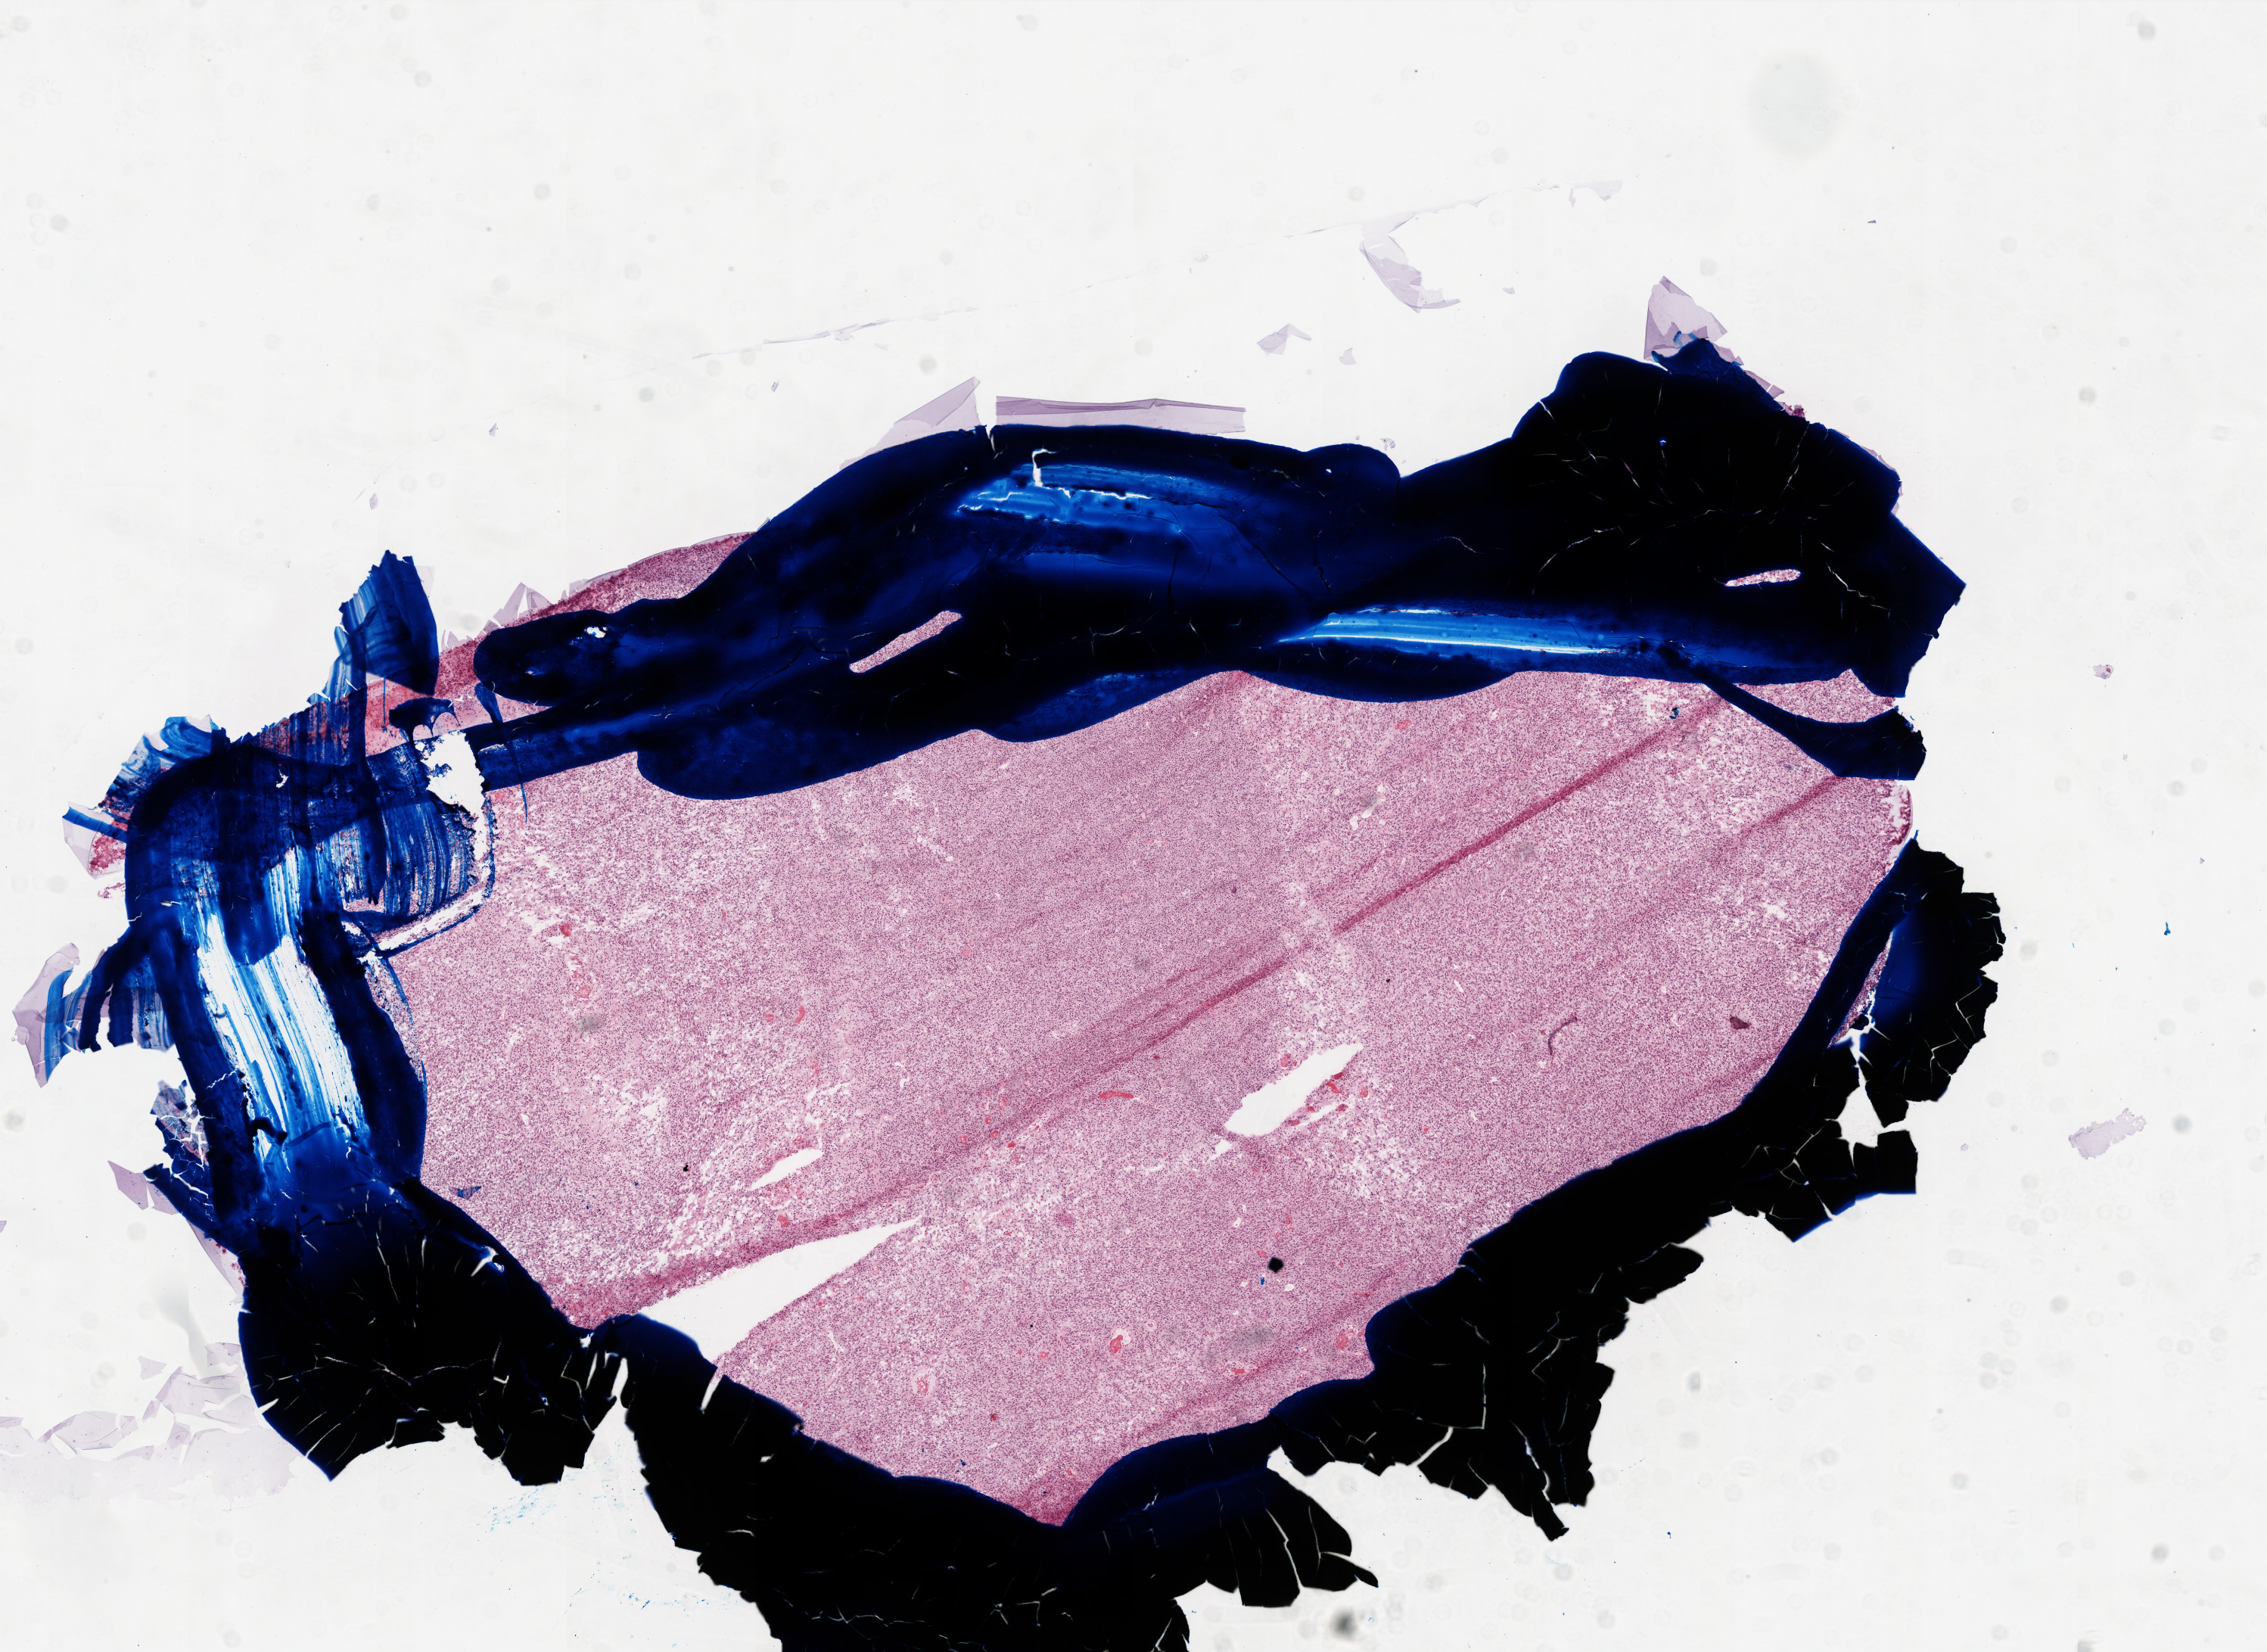
H&E whole-slide image, whole scanned area (about 12.0 x 8.7 mm) shown as a low-resolution overview; frozen section; primary tumour sample from the brain. Female patient; age at initial diagnosis 63 years. Pathologist review of this section (percent, as recorded): tumour cells 90%, tumour nuclei 100%, normal cells 0%, stromal cells 0%, necrosis 10%. Inflammatory infiltration, as recorded: lymphocyte infiltration 0%, monocyte infiltration 0%, neutrophil infiltration 0%.
• diagnosis: Glioblastoma